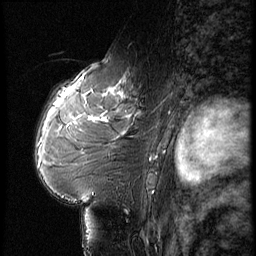
Breast MRI (dynamic contrast-enhanced), one sagittal slice; position 38 of 56 along the scan axis; dynamic contrast-enhanced series, image 2 of 3 at this slice position (ordered by acquisition); 1.5 T; TE 4.2 ms, TR 9 ms; 2.5 mm slice thickness; 256 × 256 image matrix, field of view 180 × 180 mm. Patient: female, 61 years. From the clinical record (not read from this slice): setting: breast cancer imaged before/during neoadjuvant chemotherapy; receptor status: HR-positive, HER2-negative.
Annotated regions visible in this slice (semi-automatically segmented with operator editing):
- analysis volume of interest (the breast-tissue region the enhancement analysis was run in; not a lesion): bounding box (x1, y1, x2, y2) in pixels: (65, 74, 149, 175)
- tumour enhancement mask (voxels above the 140 % enhancement threshold inside the analysis volume of interest): (68, 90, 125, 127)